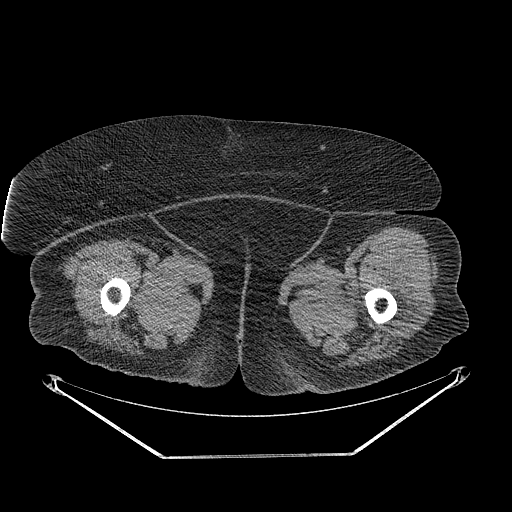
CT of an extremity soft-tissue mass (from a PET/CT study), one axial slice; slice 257 of 267 in the series (ordered by position); reconstruction kernel STANDARD; 140 kVp; soft-tissue window (W 400 / L 40 HU); 3.75 mm slice thickness; 512 × 512 image matrix. Female patient. Case-level facts recorded for this patient, not image findings: histological type: undifferentiated – high grade; grade: high; site of the primary tumour: left thigh.
Structures marked on this image (expert contour drawn on MRI and transferred to this co-registered scan by the dataset authors):
- gross tumour volume including surrounding oedema: bounding box (x1, y1, x2, y2) in pixels: (386, 281, 419, 334)
- gross tumour volume (mass): (397, 311, 410, 316)